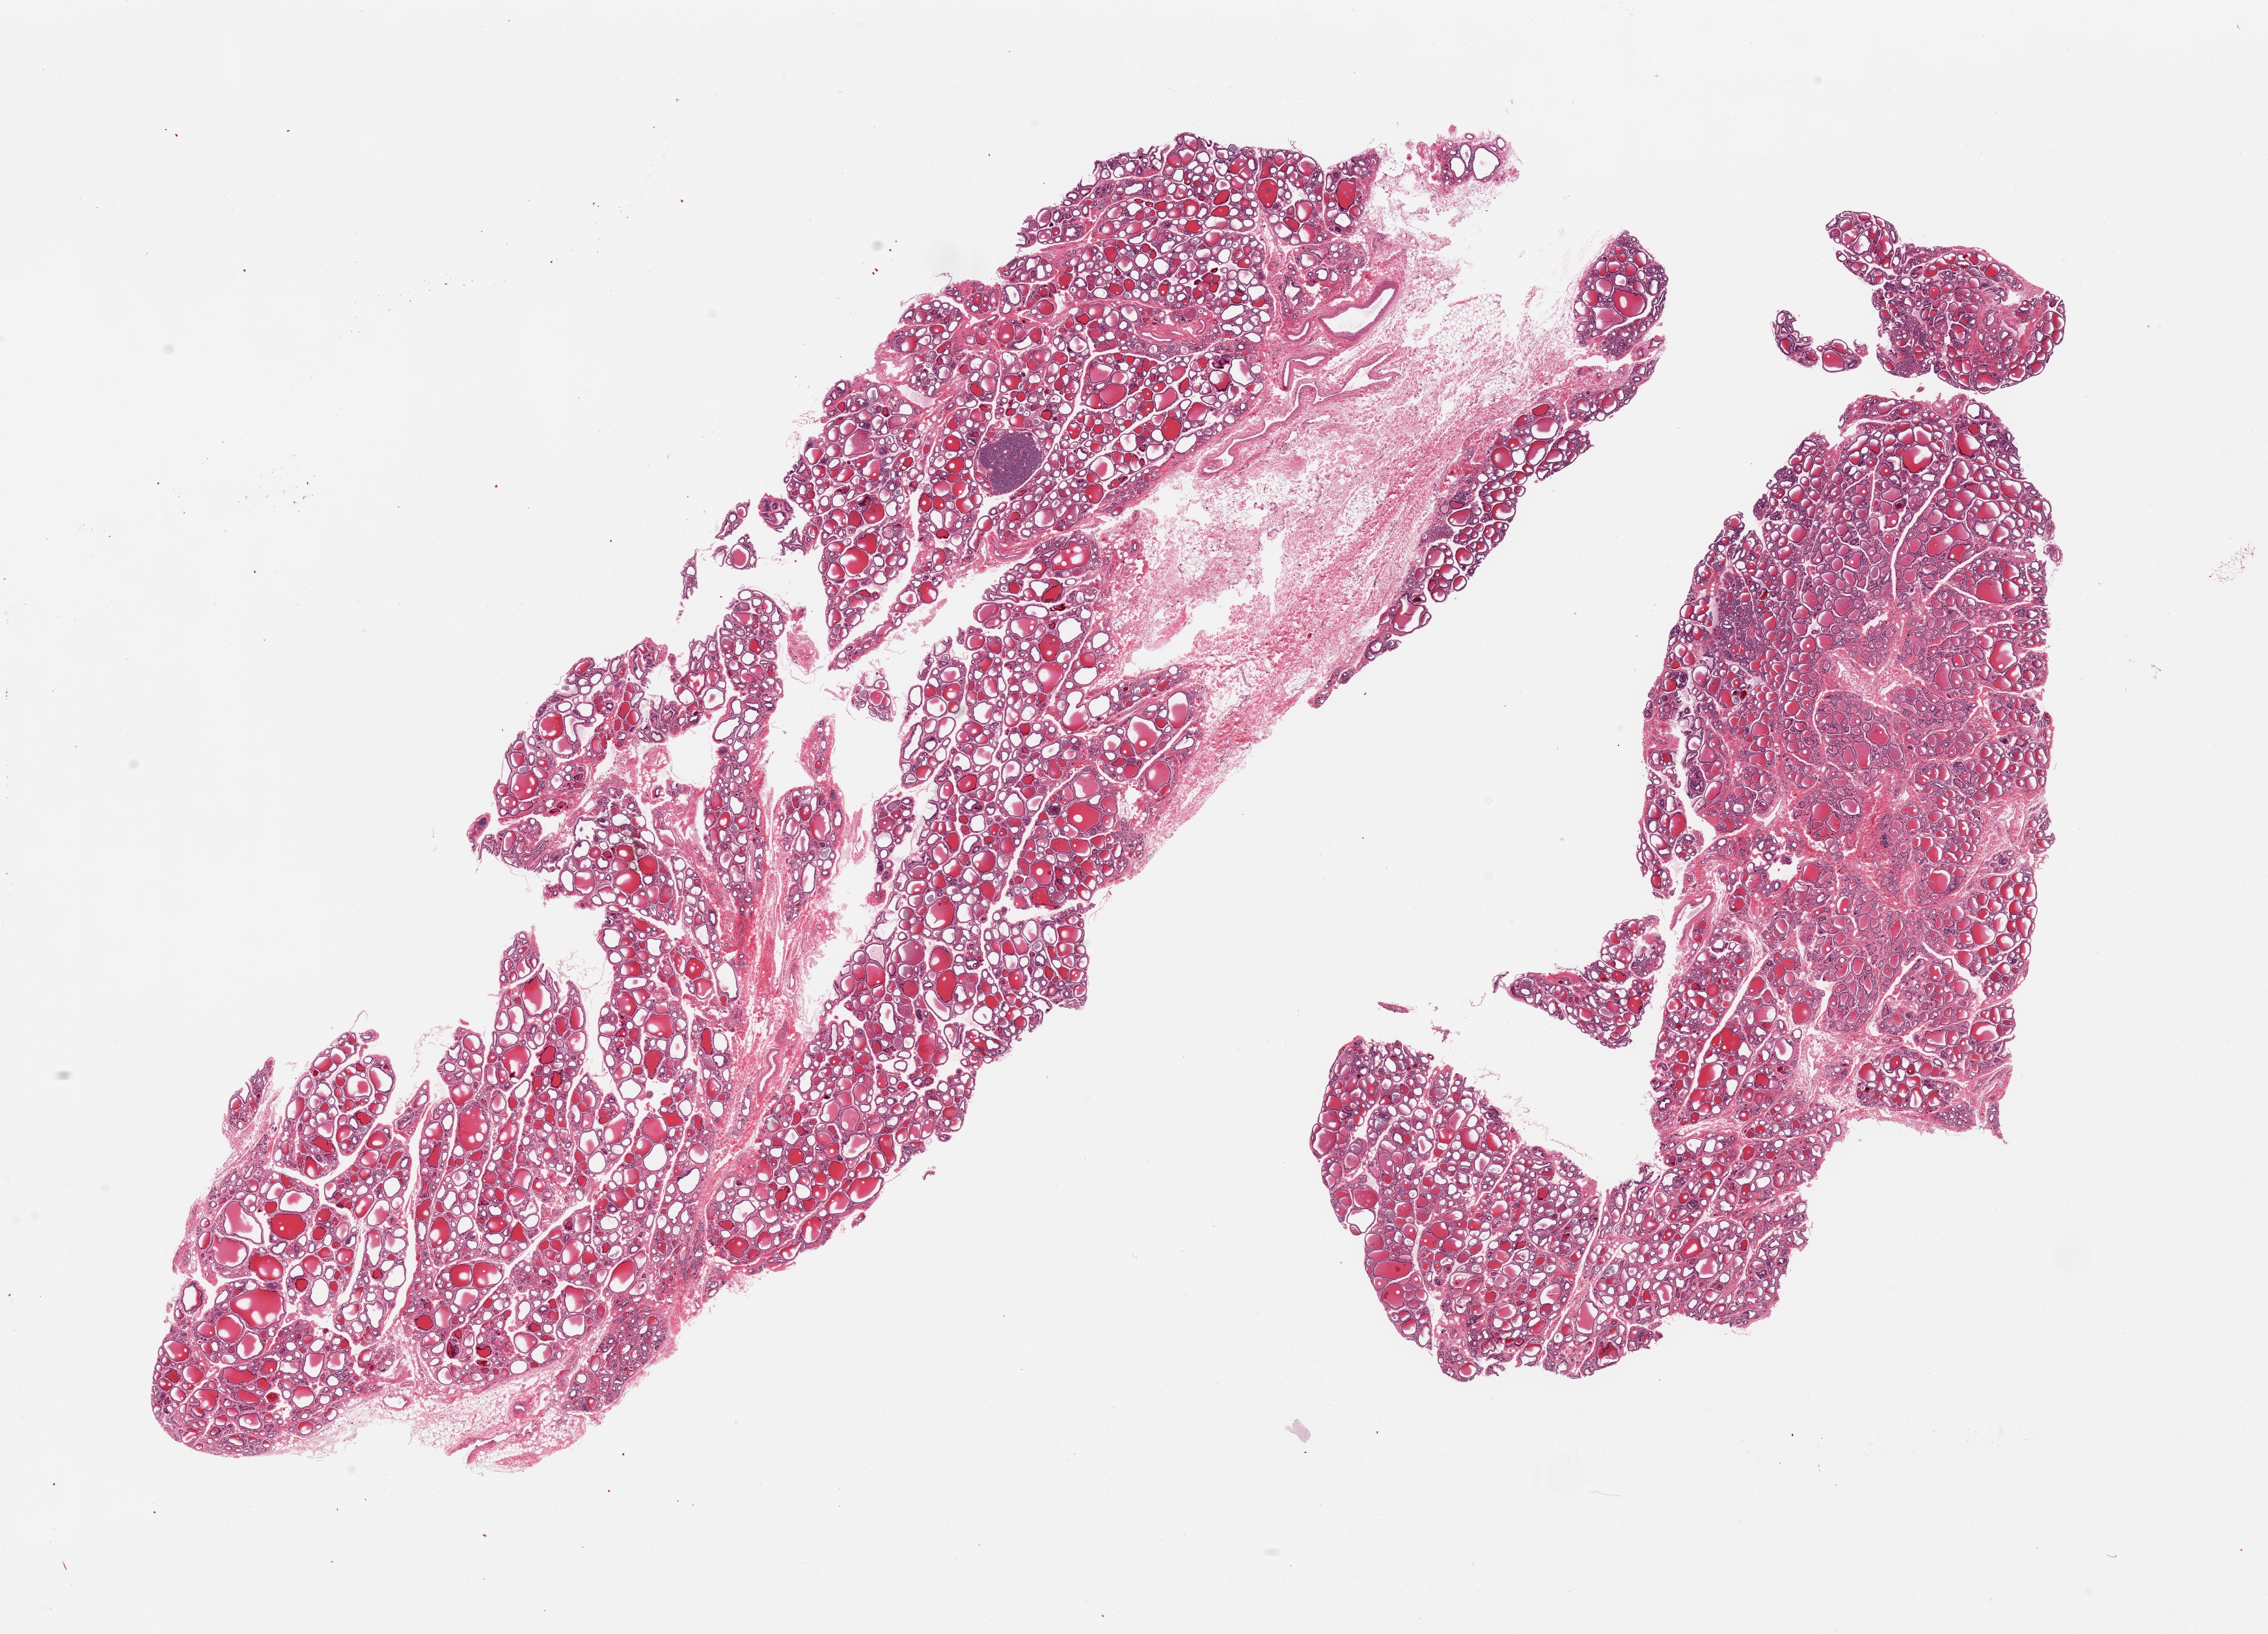
Hematoxylin and eosin (H&E) whole-slide image — whole scanned area (about 27.6 x 19.9 mm) shown as a low-resolution overview, PAXgene-fixed paraffin-embedded (PFPE) section, target tissue: thyroid, tissue donor sample. Donor sex: male.
• reviewer comment on this tissue sample: 2 pieces; some fibrosis and nodularity; one piece is ~20% fat, fibrocollagenous tissue and large vessels; small adenomatoid nodule